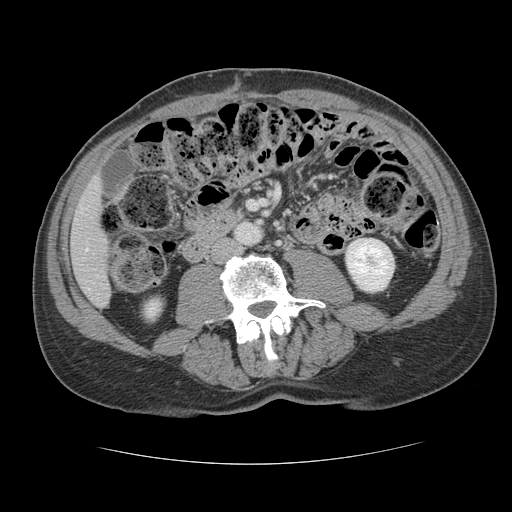
Contrast-enhanced abdominal CT, one axial slice. Reconstruction kernel STANDARD. 120 kVp. Intravenous contrast given. Soft-tissue window (W 400 / L 40 HU). 512 × 512 image matrix, field of view 377 × 377 mm. Male patient, age 68 years. From the clinical record (not read from this slice): diagnosis: colorectal cancer liver metastases, imaged before liver resection; multiple liver metastases: yes; largest metastasis: 2.2 cm; chemotherapy before resection: no.
Outlined on this slice (expert manual segmentation):
- hepatic veins: bounding box (x1, y1, x2, y2) in pixels: (86, 248, 88, 250)
- liver: (72, 181, 111, 307)
- planned liver remnant (the part of the liver to remain after resection): (72, 180, 111, 307)